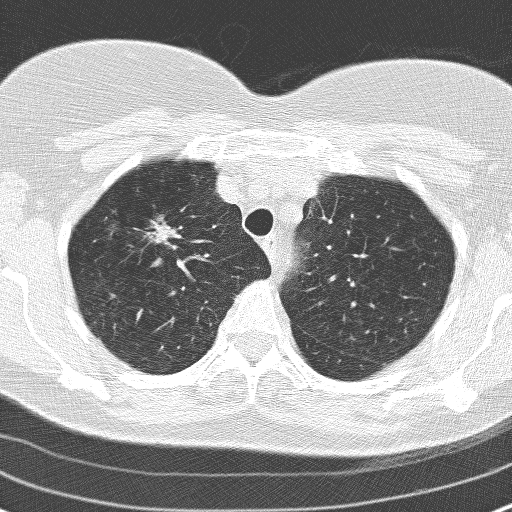
Axial slice from a low-dose chest CT screening exam, second screening round (one year after baseline), lung window (W 1500 / L -600 HU), lung (sharp) reconstruction kernel (D), slice 35 of 160 in the series, 512 × 512 image matrix. Female, age 60 years at enrolment. Former smoker at enrolment.
Lesion marked by an expert reader, bounding box [x1, y1, x2, y2] px = [125, 208, 180, 257]. Screening reader's record for this exam (one nodule recorded; not confirmed to be the boxed lesion): non-calcified nodule or mass ≥4 mm, right upper lobe, 17 × 15 mm, spiculated (stellate) margins, soft tissue attenuation, pre-existing on the prior screen: yes; interval growth: yes. Later outcome: lung cancer diagnosed 78 days after this screen — adenocarcinoma, NOS, right upper lobe, moderately differentiated (G2), stage IA (AJCC 6th edition), 23 mm at pathology.